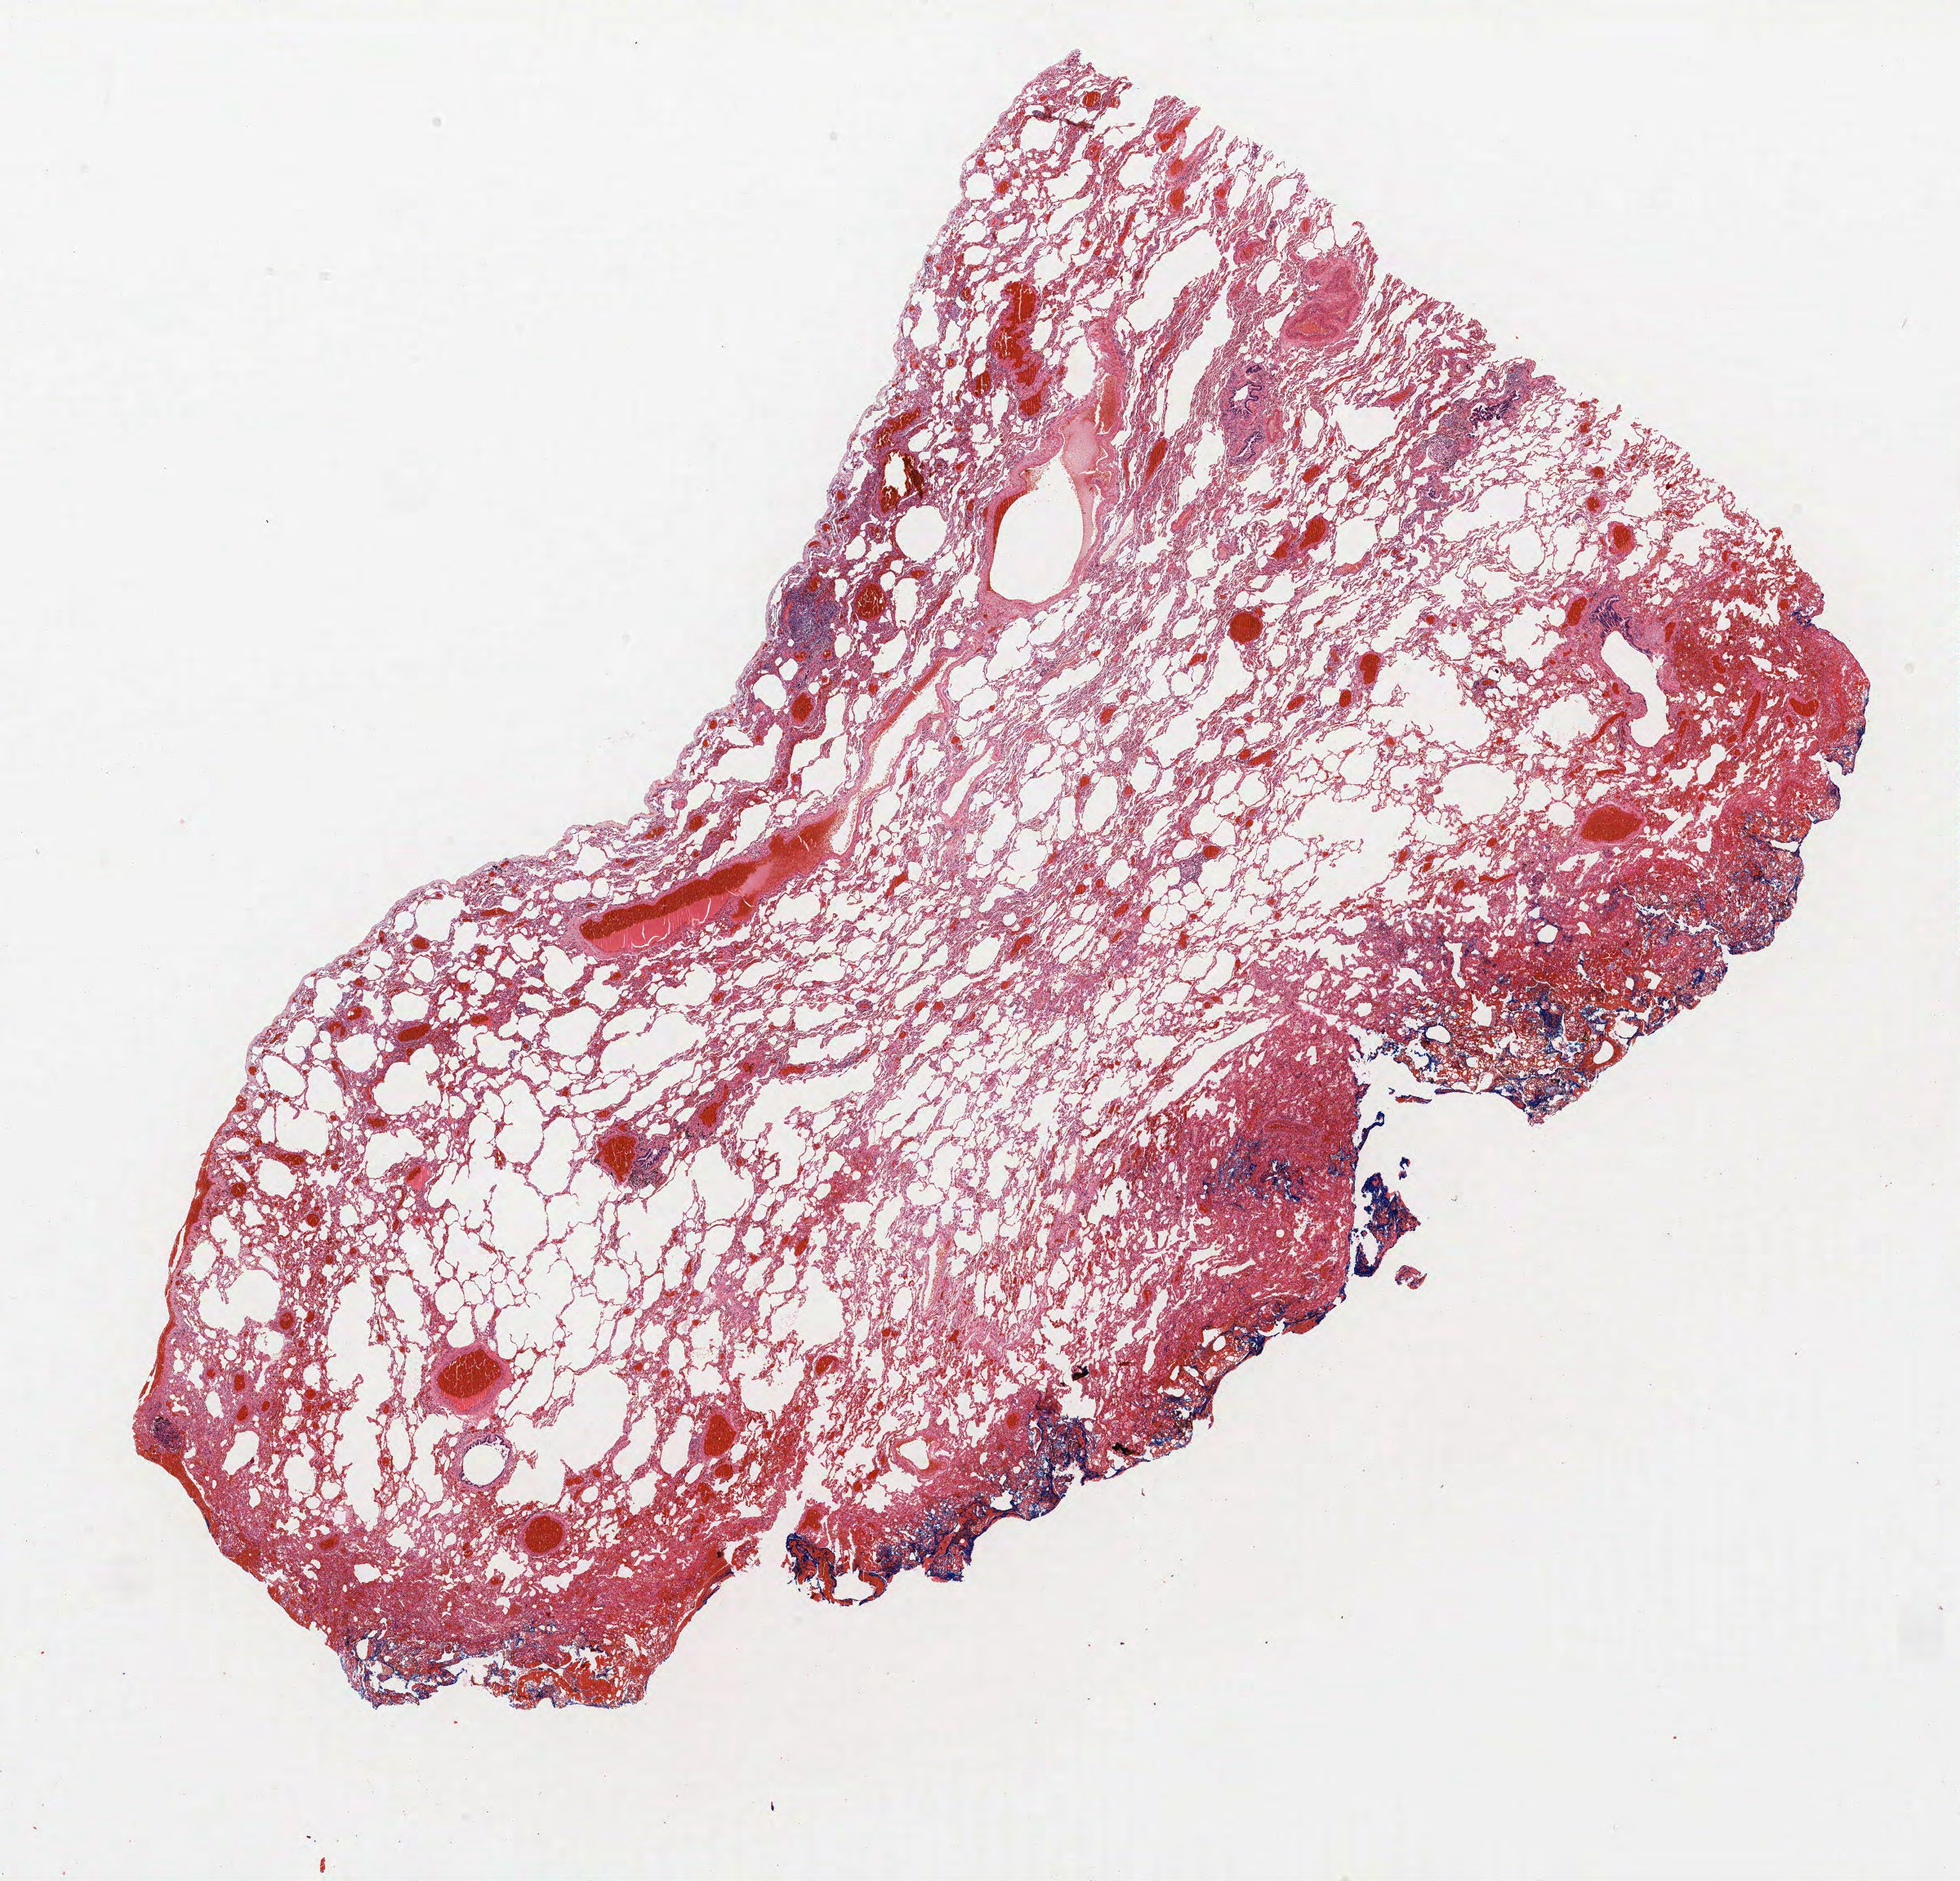
Whole-slide histology image, H&E, low-resolution overview of the scanned area, about 19.2 x 18.4 mm. Formalin-fixed paraffin-embedded (FFPE) section. Lung. Male patient, aged 56 at enrolment. Grade: poorly differentiated (G3).
* tumour size (pathology): 12 mm
* stage (AJCC 6th edition): IA
* primary tumour location (clinical record): right upper lobe
* participant's lung-cancer diagnosis: Adenocarcinoma, NOS